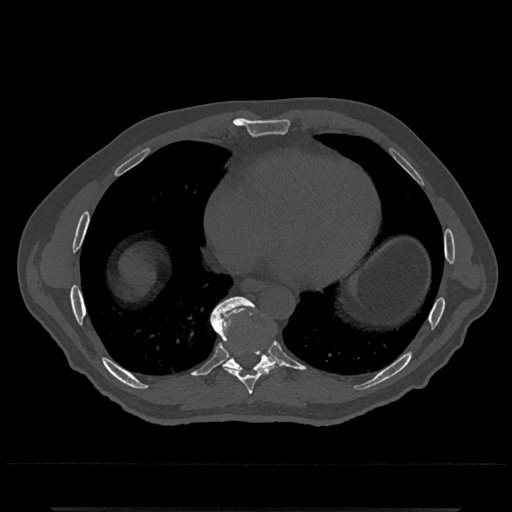
CT including the spine, one axial slice. Slice 644 of 797 in the series (ordered by position). 120 kVp. Bone window (W 1800 / L 400 HU). 0.5 mm slice thickness. 512 × 512 image matrix. Male patient, age 67 years. Case-level facts recorded for this patient, not image findings: primary cancer: prostate.
Annotated regions visible in this slice (semi-automatically segmented with operator editing):
- T8 vertebra: bounding box [x1, y1, x2, y2] px = [212, 325, 278, 395]
- T9 vertebra: [210, 297, 279, 373]